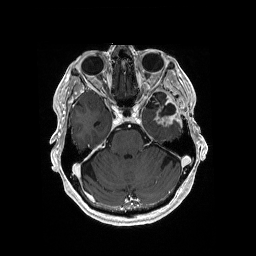
Brain MRI from a brain-tumour surgery series, one axial slice. Position 124 of 176 along the scan axis. T1-weighted post-contrast. 1 mm slice thickness. 256 × 256 image matrix, field of view 256 × 256 mm. Case-level facts recorded for this patient, not image findings: histopathology: Glioblastoma; WHO grade: 4; IDH mutation: no; tumour location: Left Medial Temporal.
Outlined on this slice (expert manual segmentation):
- previous resection cavity: bounding box <160,103,175,116> (left, top, right, bottom; pixels)
- tumour: <155,114,180,128>